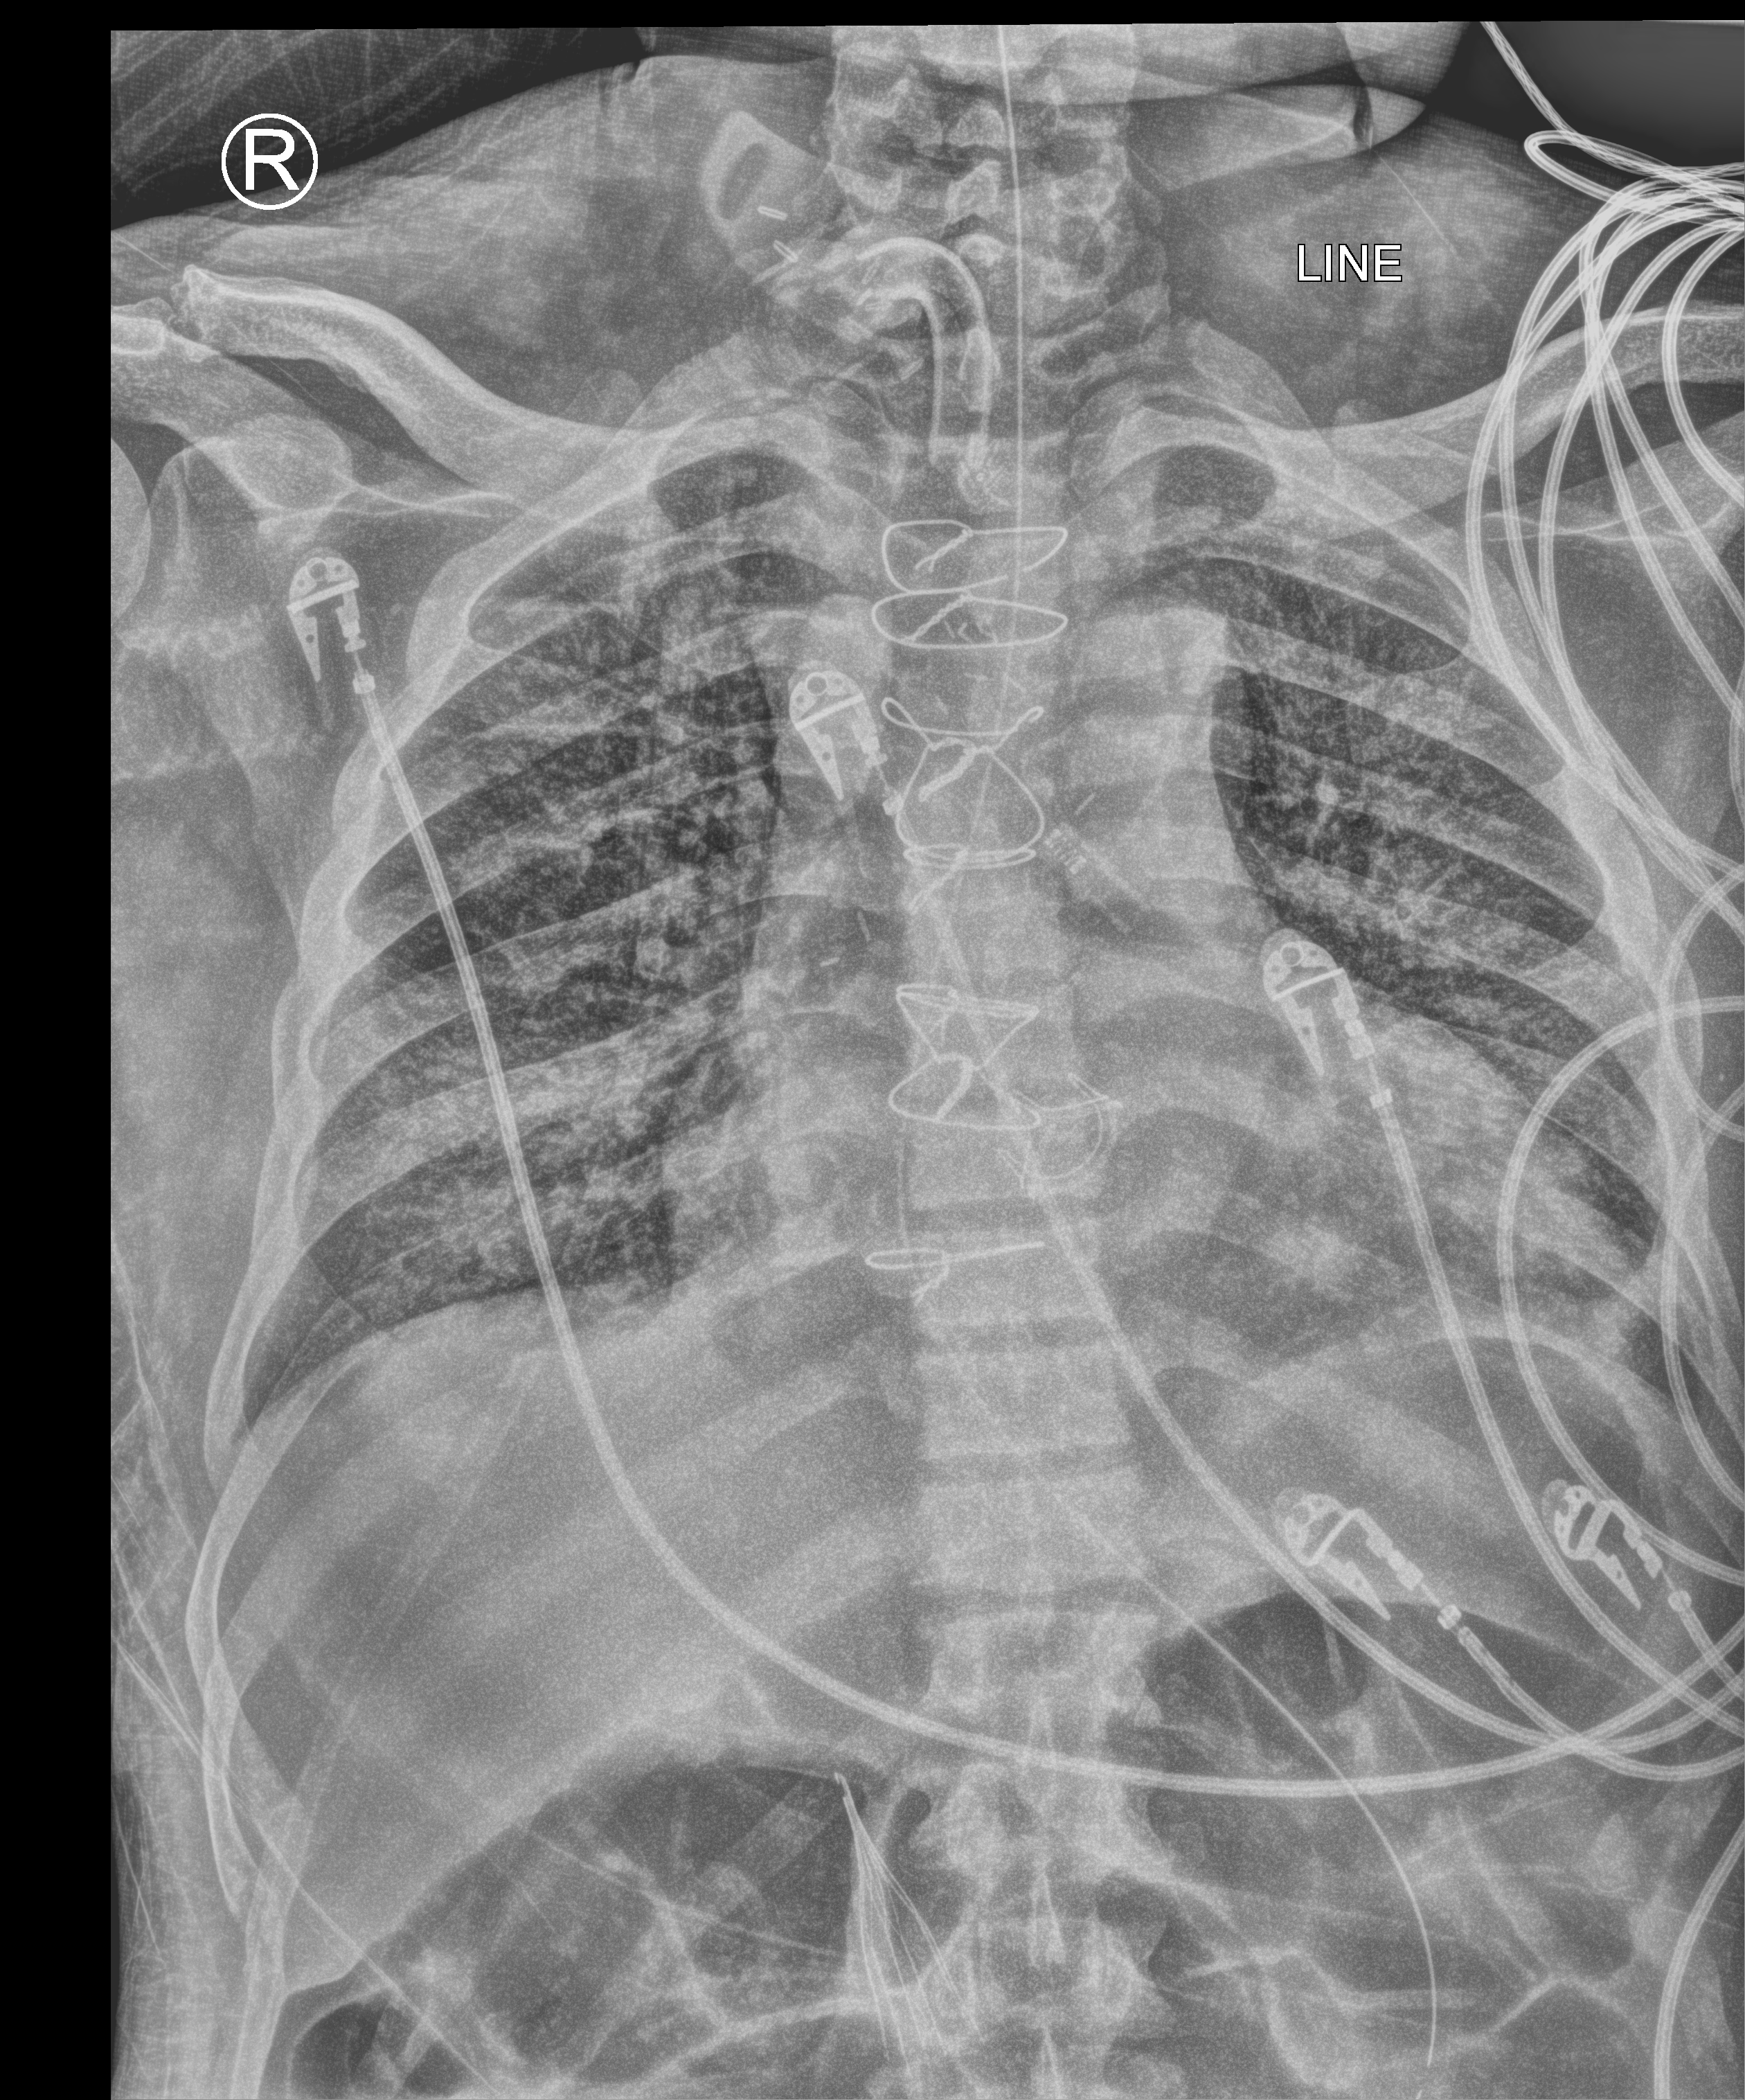
Bedside chest radiograph (computed radiography), anteroposterior (AP) projection. Male patient hospitalised with COVID-19, age 60–74 years.
Hospital-stay facts (about this admission, not read from this image; timing relative to this image not recorded): mechanically ventilated during this hospital stay: yes.